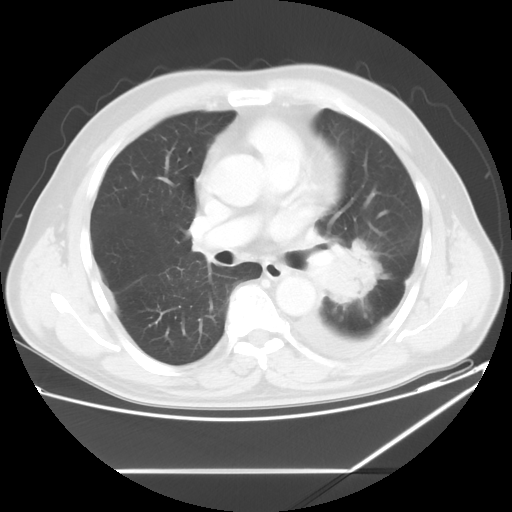
Chest CT, one axial slice. Position 33 of 60 along the scan axis. Reconstruction kernel STANDARD. Lung window (W 1500 / L -600 HU). 5 mm slice thickness. 512 × 512 image matrix. Male patient, age 62 years. From the clinical record (not read from this slice): clinical TNM (as recorded): T3 N0 M1.
Structures marked on this image (rectangle marked by the reading radiologist):
- lung tumour (recorded histology: adenocarcinoma): bounding box <319,245,376,308> (left, top, right, bottom; pixels)
- lung tumour (recorded histology: adenocarcinoma): <325,242,375,304>